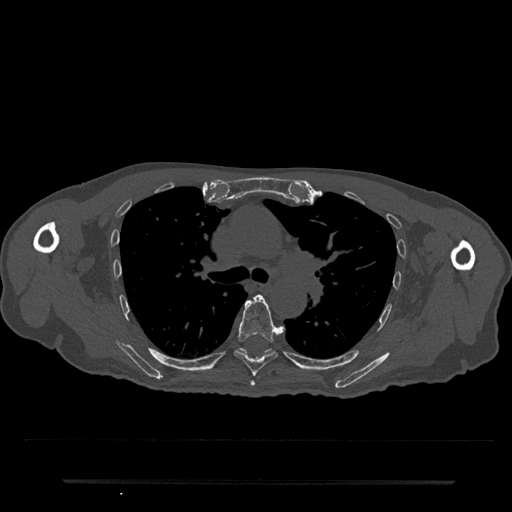
CT including the spine, one axial slice. Slice 525 of 797 in the series (ordered by position). Bone window (W 1800 / L 400 HU). 512 × 512 image matrix, field of view 427 × 427 mm. Patient: male, 74 years. From the clinical record (not read from this slice): primary cancer: prostate.
Structures marked on this image (semi-automatically segmented with operator editing):
- T5 vertebra: box from (x=250, y=380) to (x=255, y=386) px
- T6 vertebra: (x=234, y=295)–(x=284, y=377)
- T7 vertebra: (x=239, y=349)–(x=270, y=353)